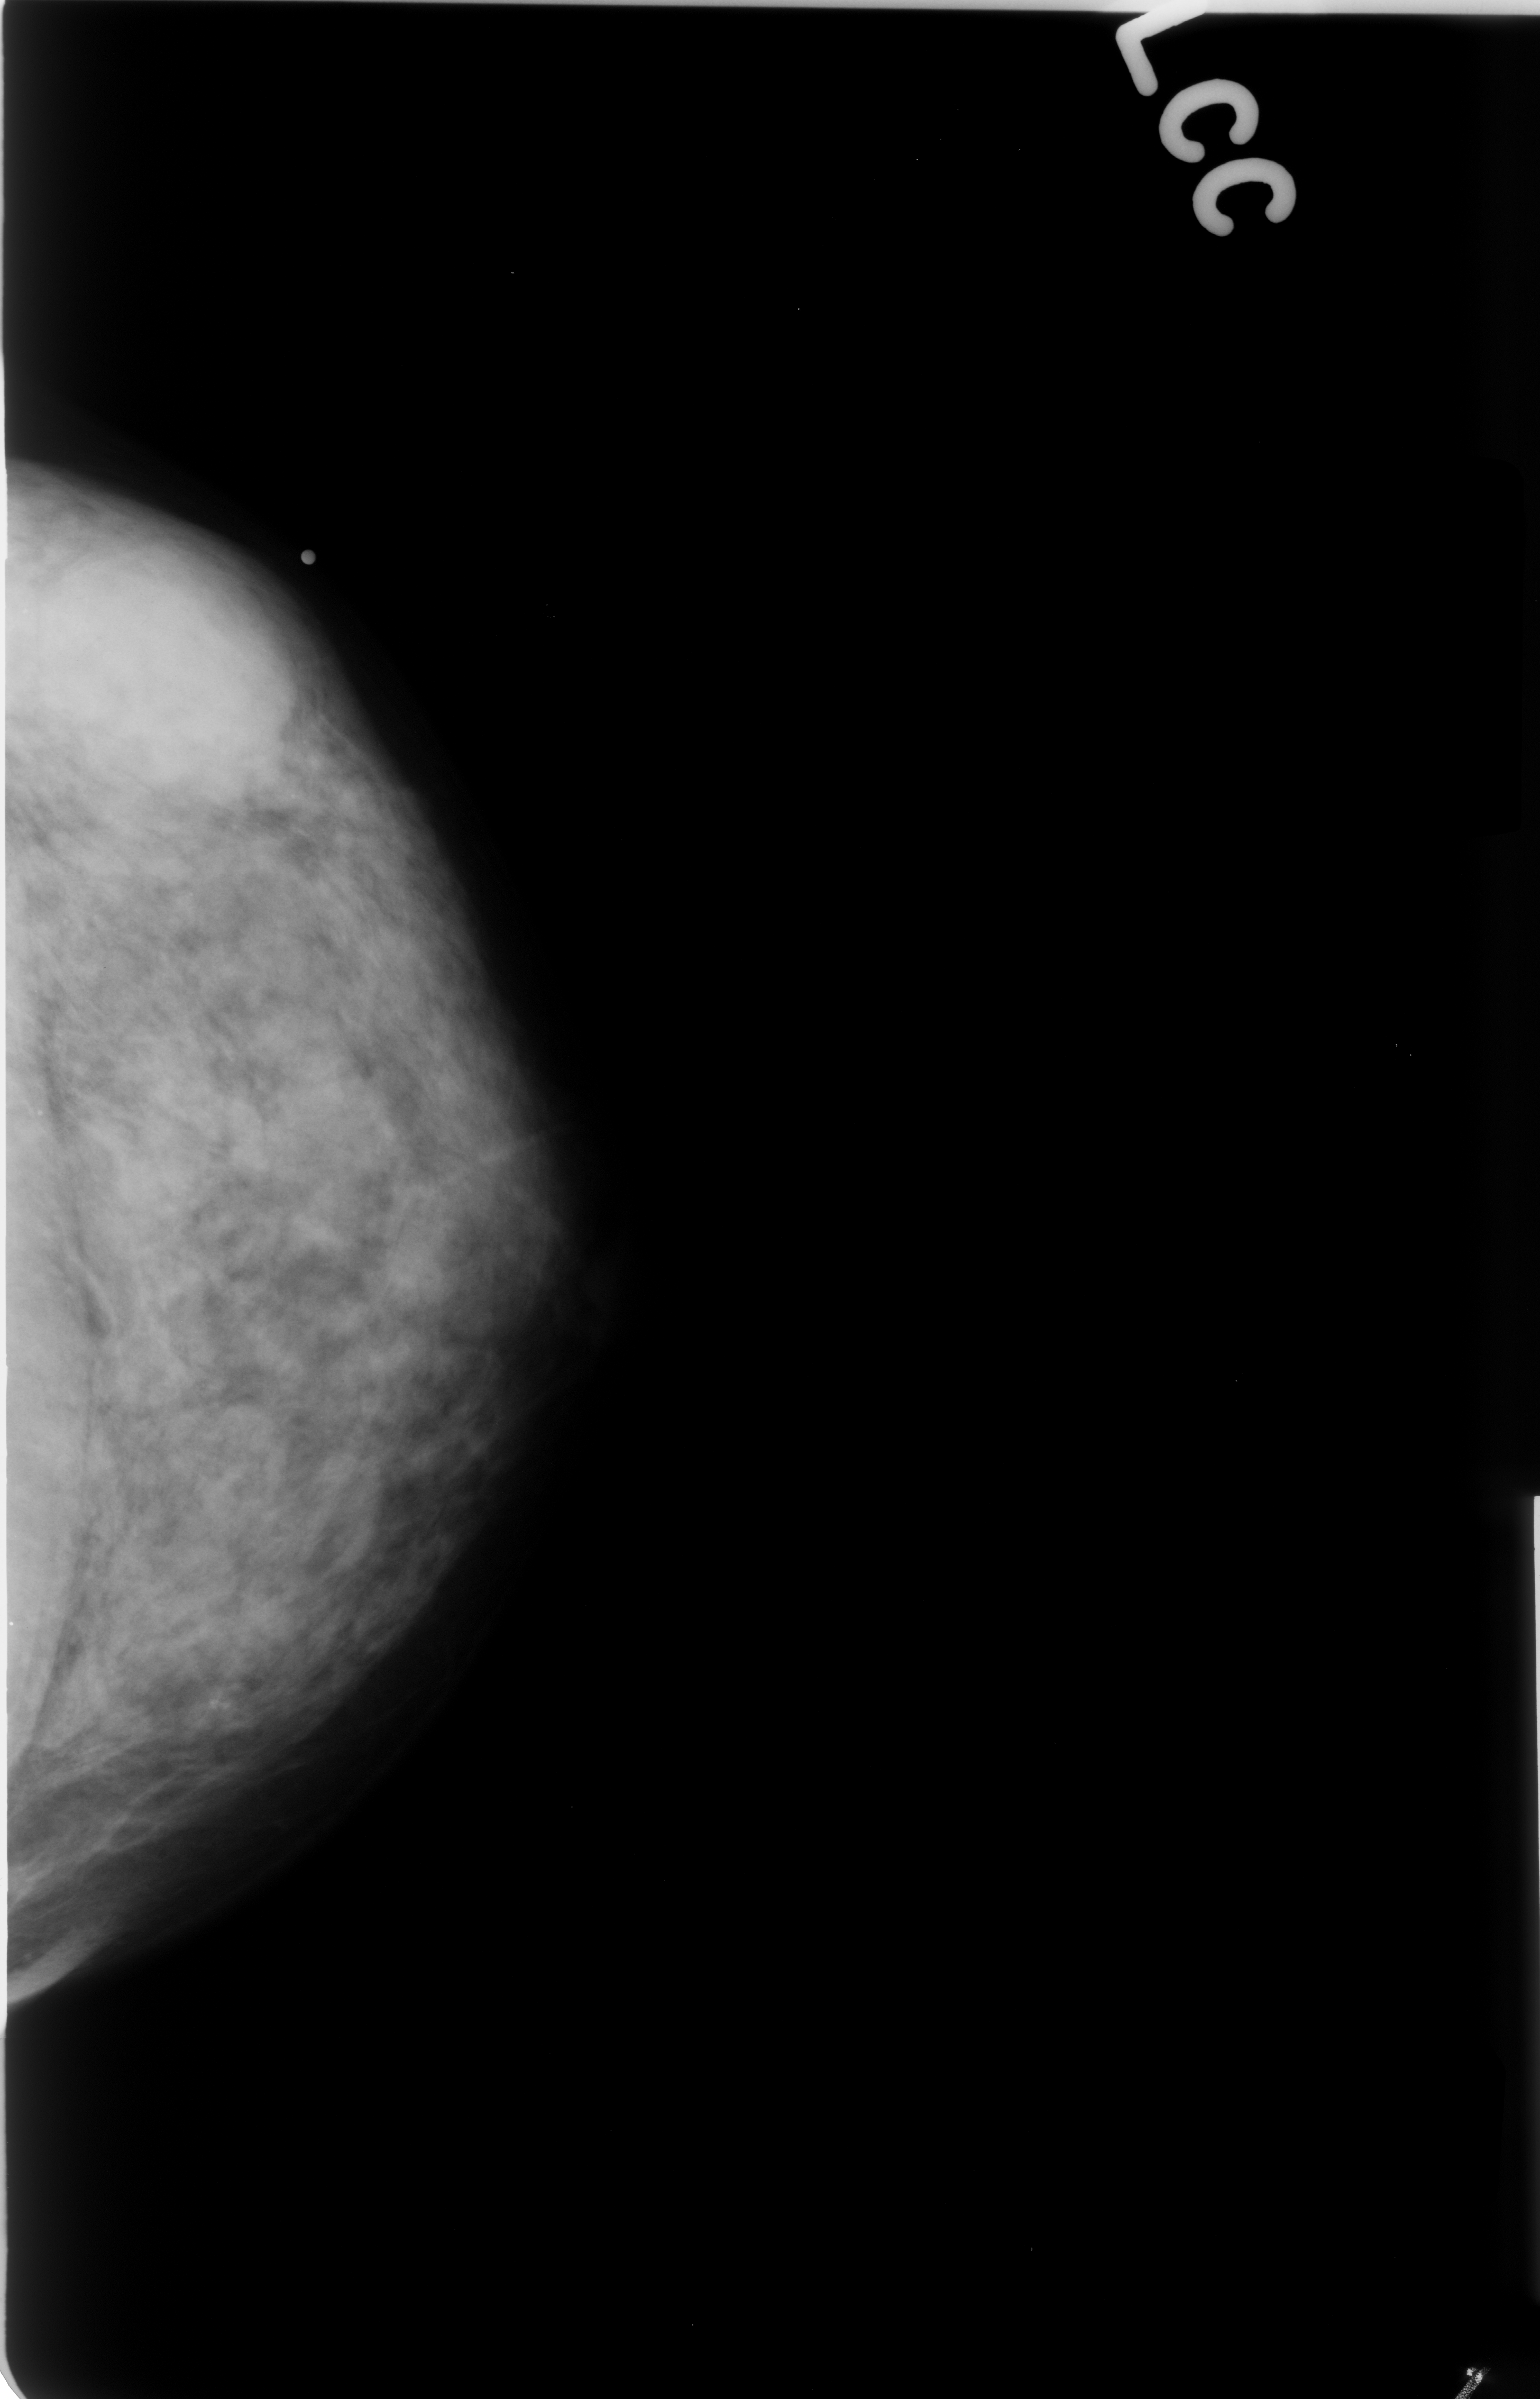
Digitized screen-film mammogram, left breast, craniocaudal (CC) view, breast composition: heterogeneously dense (BI-RADS density category 3 of 4).
- Marked findings (only marked abnormalities are described; nothing is implied about the rest of the image): calcifications, morphology dystrophic, distribution clustered; BI-RADS assessment category 3; pathology result (as recorded, not read from the image): benign.